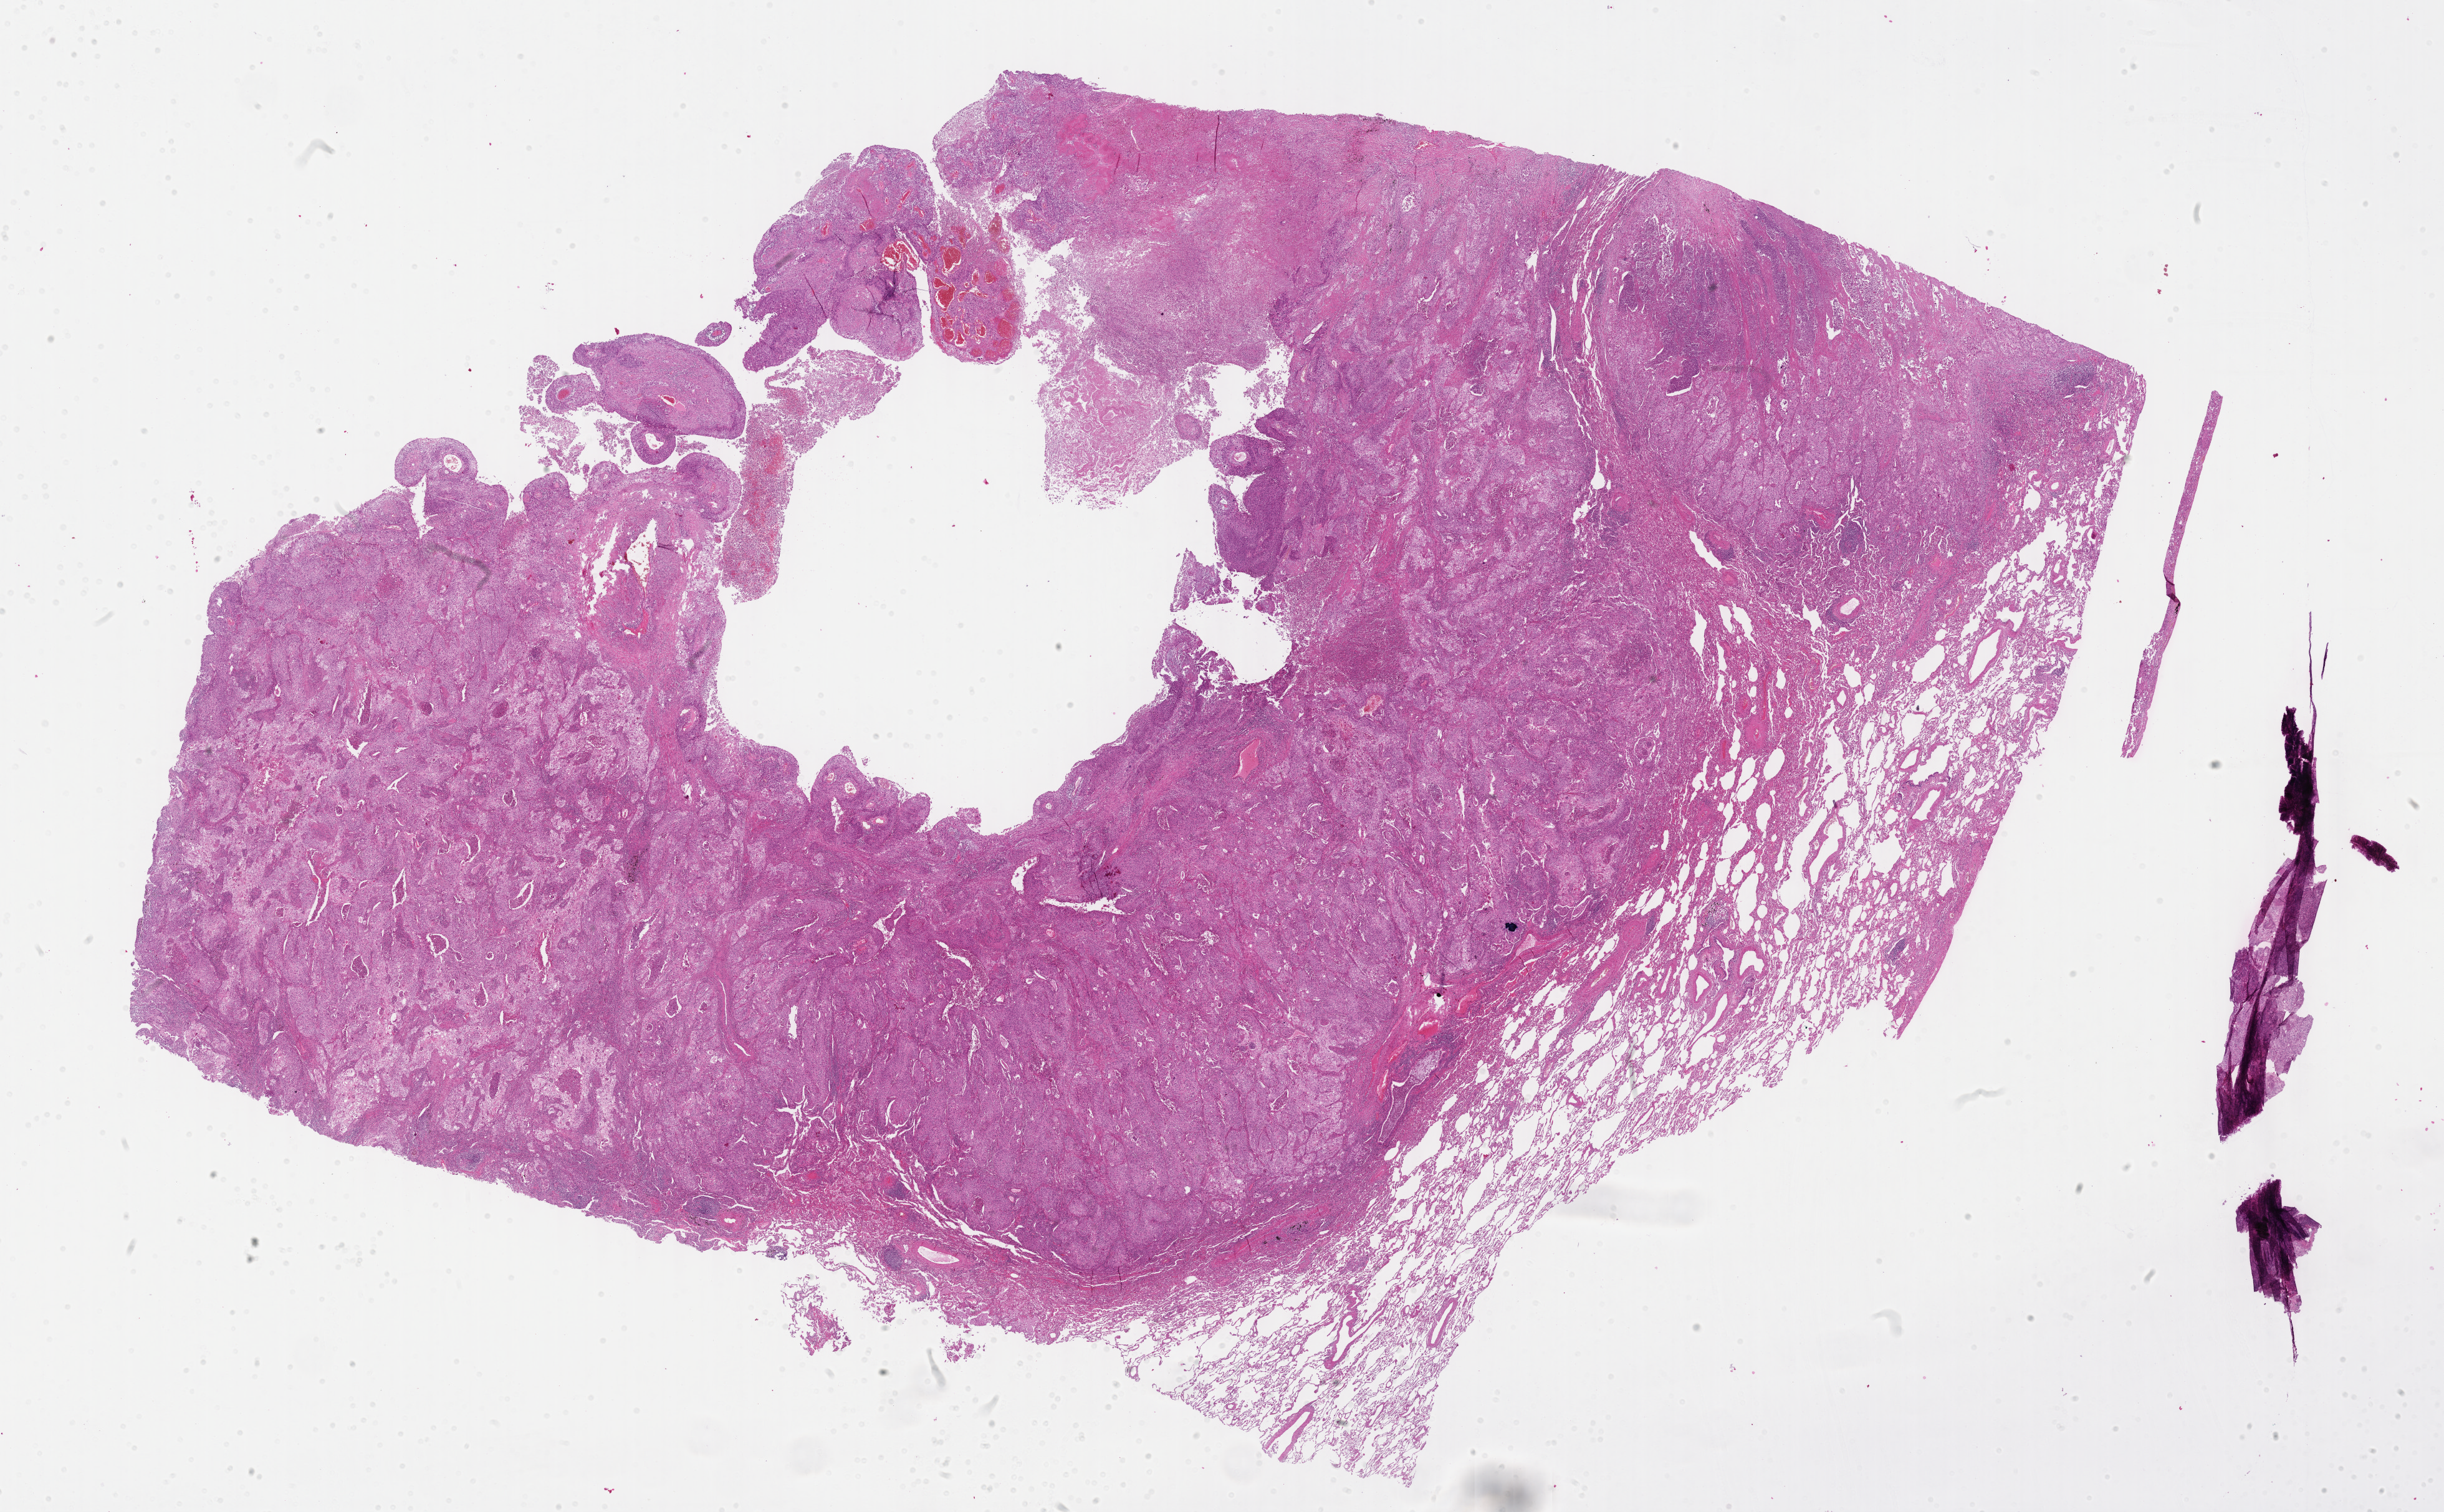
Whole-slide histology image, H&E-stained — a low-resolution overview of the entire scanned area, about 31.7 x 19.6 mm (acquisition: 40x scan), FFPE section, sample: primary tumour, lung. Male, age 76 years at initial diagnosis.
Pathologic diagnosis: Squamous cell carcinoma, NOS. AJCC pathologic stage: IB.